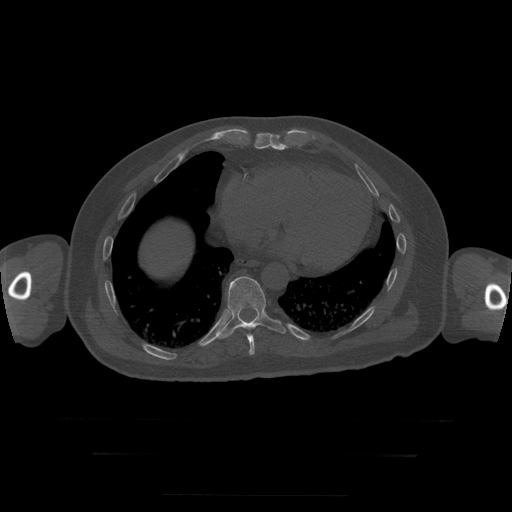
CT including the spine, one axial slice. Position 128 of 397 along the scan axis. Reconstruction kernel STANDARD. Bone window (W 1800 / L 400 HU). 1.25 mm slice thickness. 512 × 512 image matrix, field of view 510 × 510 mm. Patient age 73 years. Case-level facts recorded for this patient, not image findings: primary cancer: prostate.
Annotated regions visible in this slice (semi-automatically segmented with operator editing):
- T10 vertebra: bounding box [x1, y1, x2, y2] px = [217, 277, 286, 339]
- T9 vertebra: [247, 334, 255, 356]